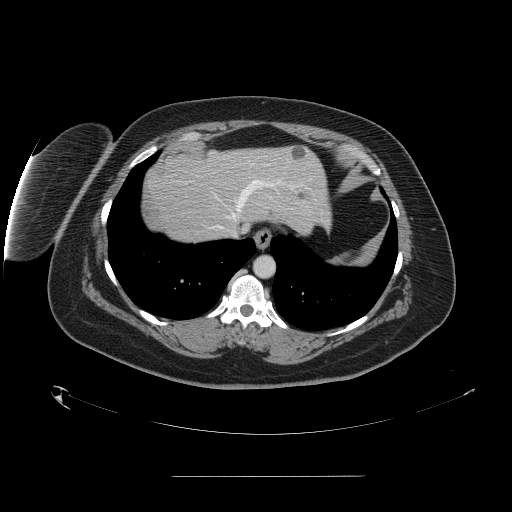
Contrast-enhanced abdominal CT, one axial slice; slice 134 of 164 in the series (ordered by position); 120 kVp; intravenous contrast given; soft-tissue window (W 400 / L 40 HU); 2.5 mm slice thickness; 512 × 512 image matrix. Female patient, age 52 years. Case-level facts recorded for this patient, not image findings: diagnosis: colorectal cancer liver metastases, imaged before liver resection; multiple liver metastases: yes; largest metastasis: 3.5 cm; disease in both lobes: no.
Outlined on this slice (outlined manually by an expert reader):
- hepatic veins: box from (x=218, y=163) to (x=281, y=237) px
- liver: (x=147, y=146)–(x=329, y=243)
- planned liver remnant (the part of the liver to remain after resection): (x=174, y=146)–(x=330, y=229)
- liver metastasis: (x=300, y=194)–(x=304, y=198)
- liver metastasis: (x=269, y=213)–(x=272, y=216)
- liver metastasis: (x=290, y=148)–(x=307, y=160)